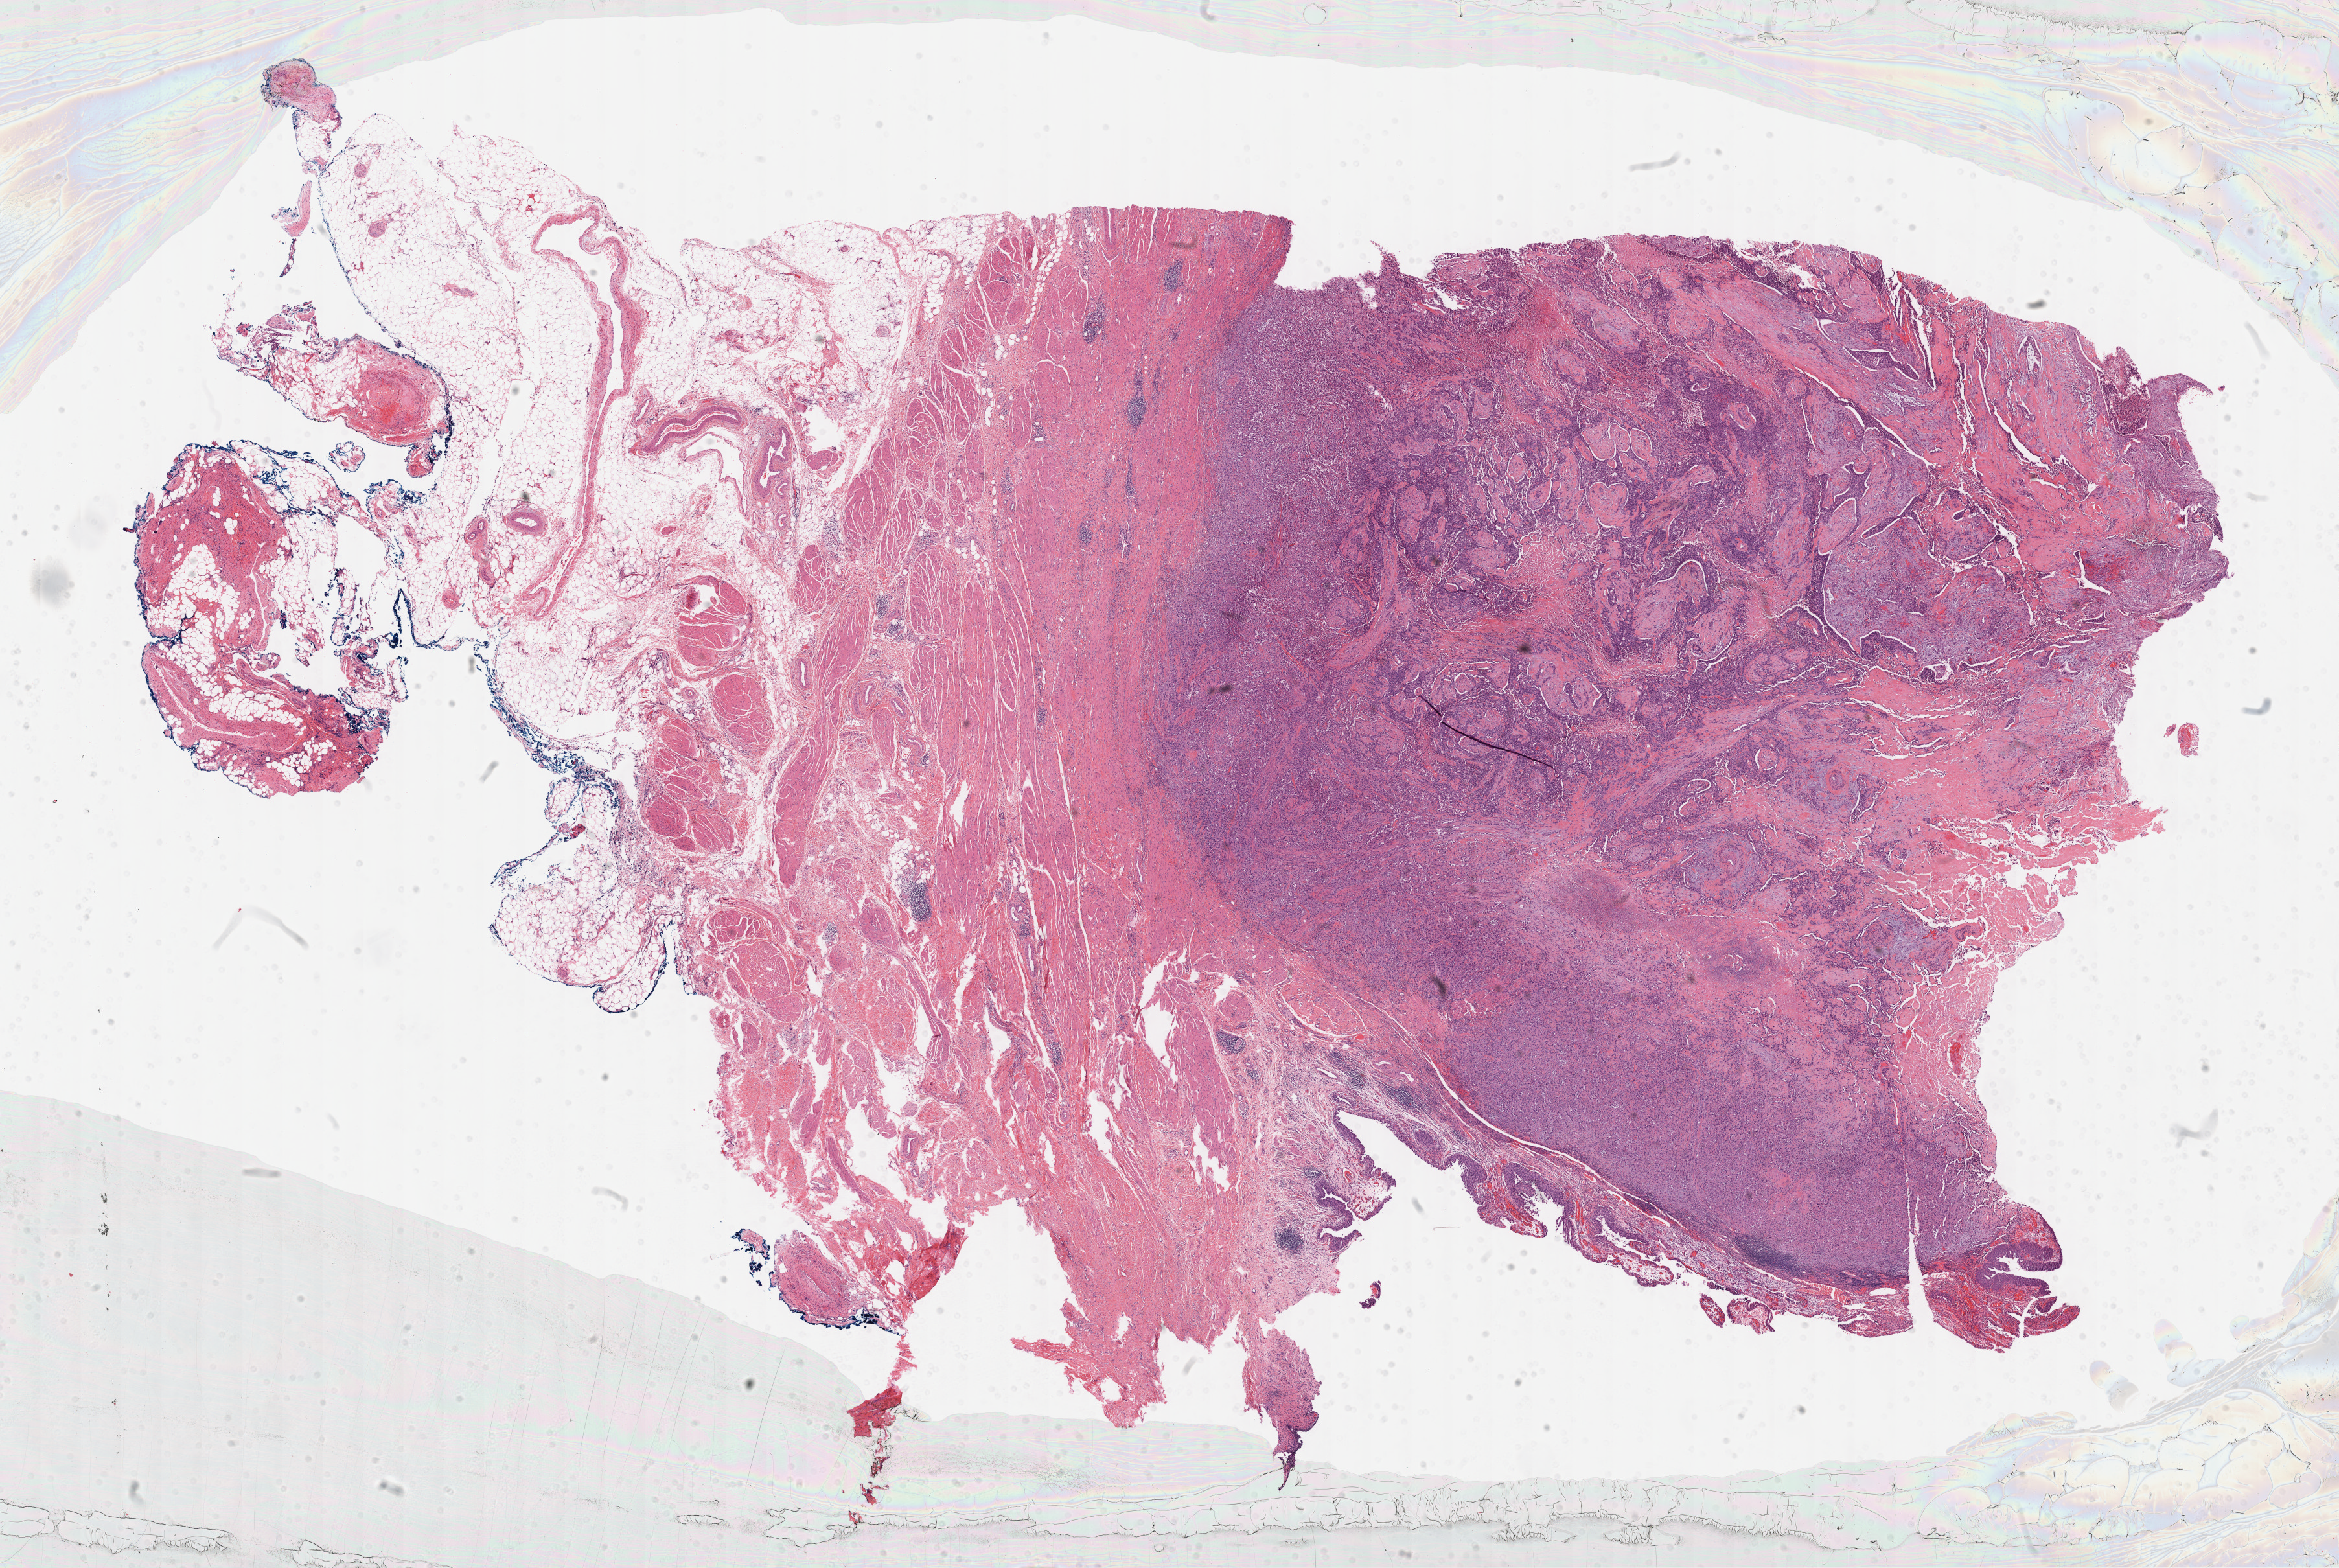
Whole-slide histology image, Hematoxylin and eosin (H&E) stained, low-resolution overview of the scanned area, about 29.2 x 19.6 mm (slide scanned at 40x), FFPE section, bladder, primary tumour sample. Male patient. Histologic grade: high grade.
Histologic diagnosis: Transitional cell carcinoma. AJCC pathologic stage: IV.